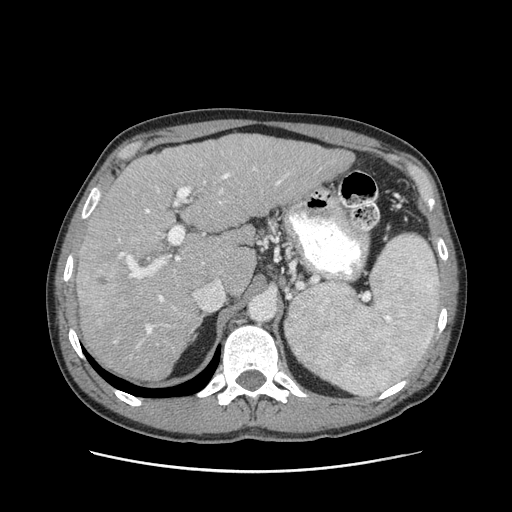
Contrast-enhanced abdominal CT (liver protocol), one axial slice; position 63 of 93 along the scan axis; 120 kVp; soft-tissue window (W 400 / L 40 HU); 2.5 mm slice thickness; 512 × 512 image matrix, field of view 380 × 380 mm. From the clinical record (not read from this slice): diagnosis: hepatocellular carcinoma (patient treated with transarterial chemoembolisation; whether this scan precedes or follows treatment is not stated here); TNM stage (as recorded): Stage-II; Child-Pugh class: A; tumour differentiation: moderately differentiated; tumour nodularity: multinodular.
Annotated regions visible in this slice (semi-automatically segmented with operator editing):
- liver parenchyma outside the tumour (the mass and vessels are separate outlines, so this box may not span the whole liver): bounding box (x1, y1, x2, y2) in pixels: (76, 134, 353, 380)
- mass: (87, 264, 120, 300)
- liver vessels: (114, 168, 288, 347)